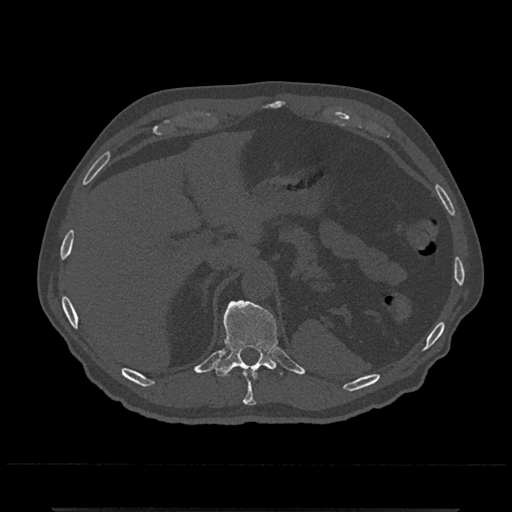
CT including the spine, one axial slice. Slice 508 of 797 in the series (ordered by position). Reconstruction kernel Br40s/3. 120 kVp. Bone window (W 1800 / L 400 HU). 0.5 mm slice thickness. 512 × 512 image matrix, field of view 393 × 393 mm. Patient: male, 67 years. Case-level facts recorded for this patient, not image findings: primary cancer: prostate.
Outlined on this slice (semi-automatically segmented with operator editing):
- T10 vertebra: bounding box <243,372,257,406> (left, top, right, bottom; pixels)
- T11 vertebra: <213,300,283,378>